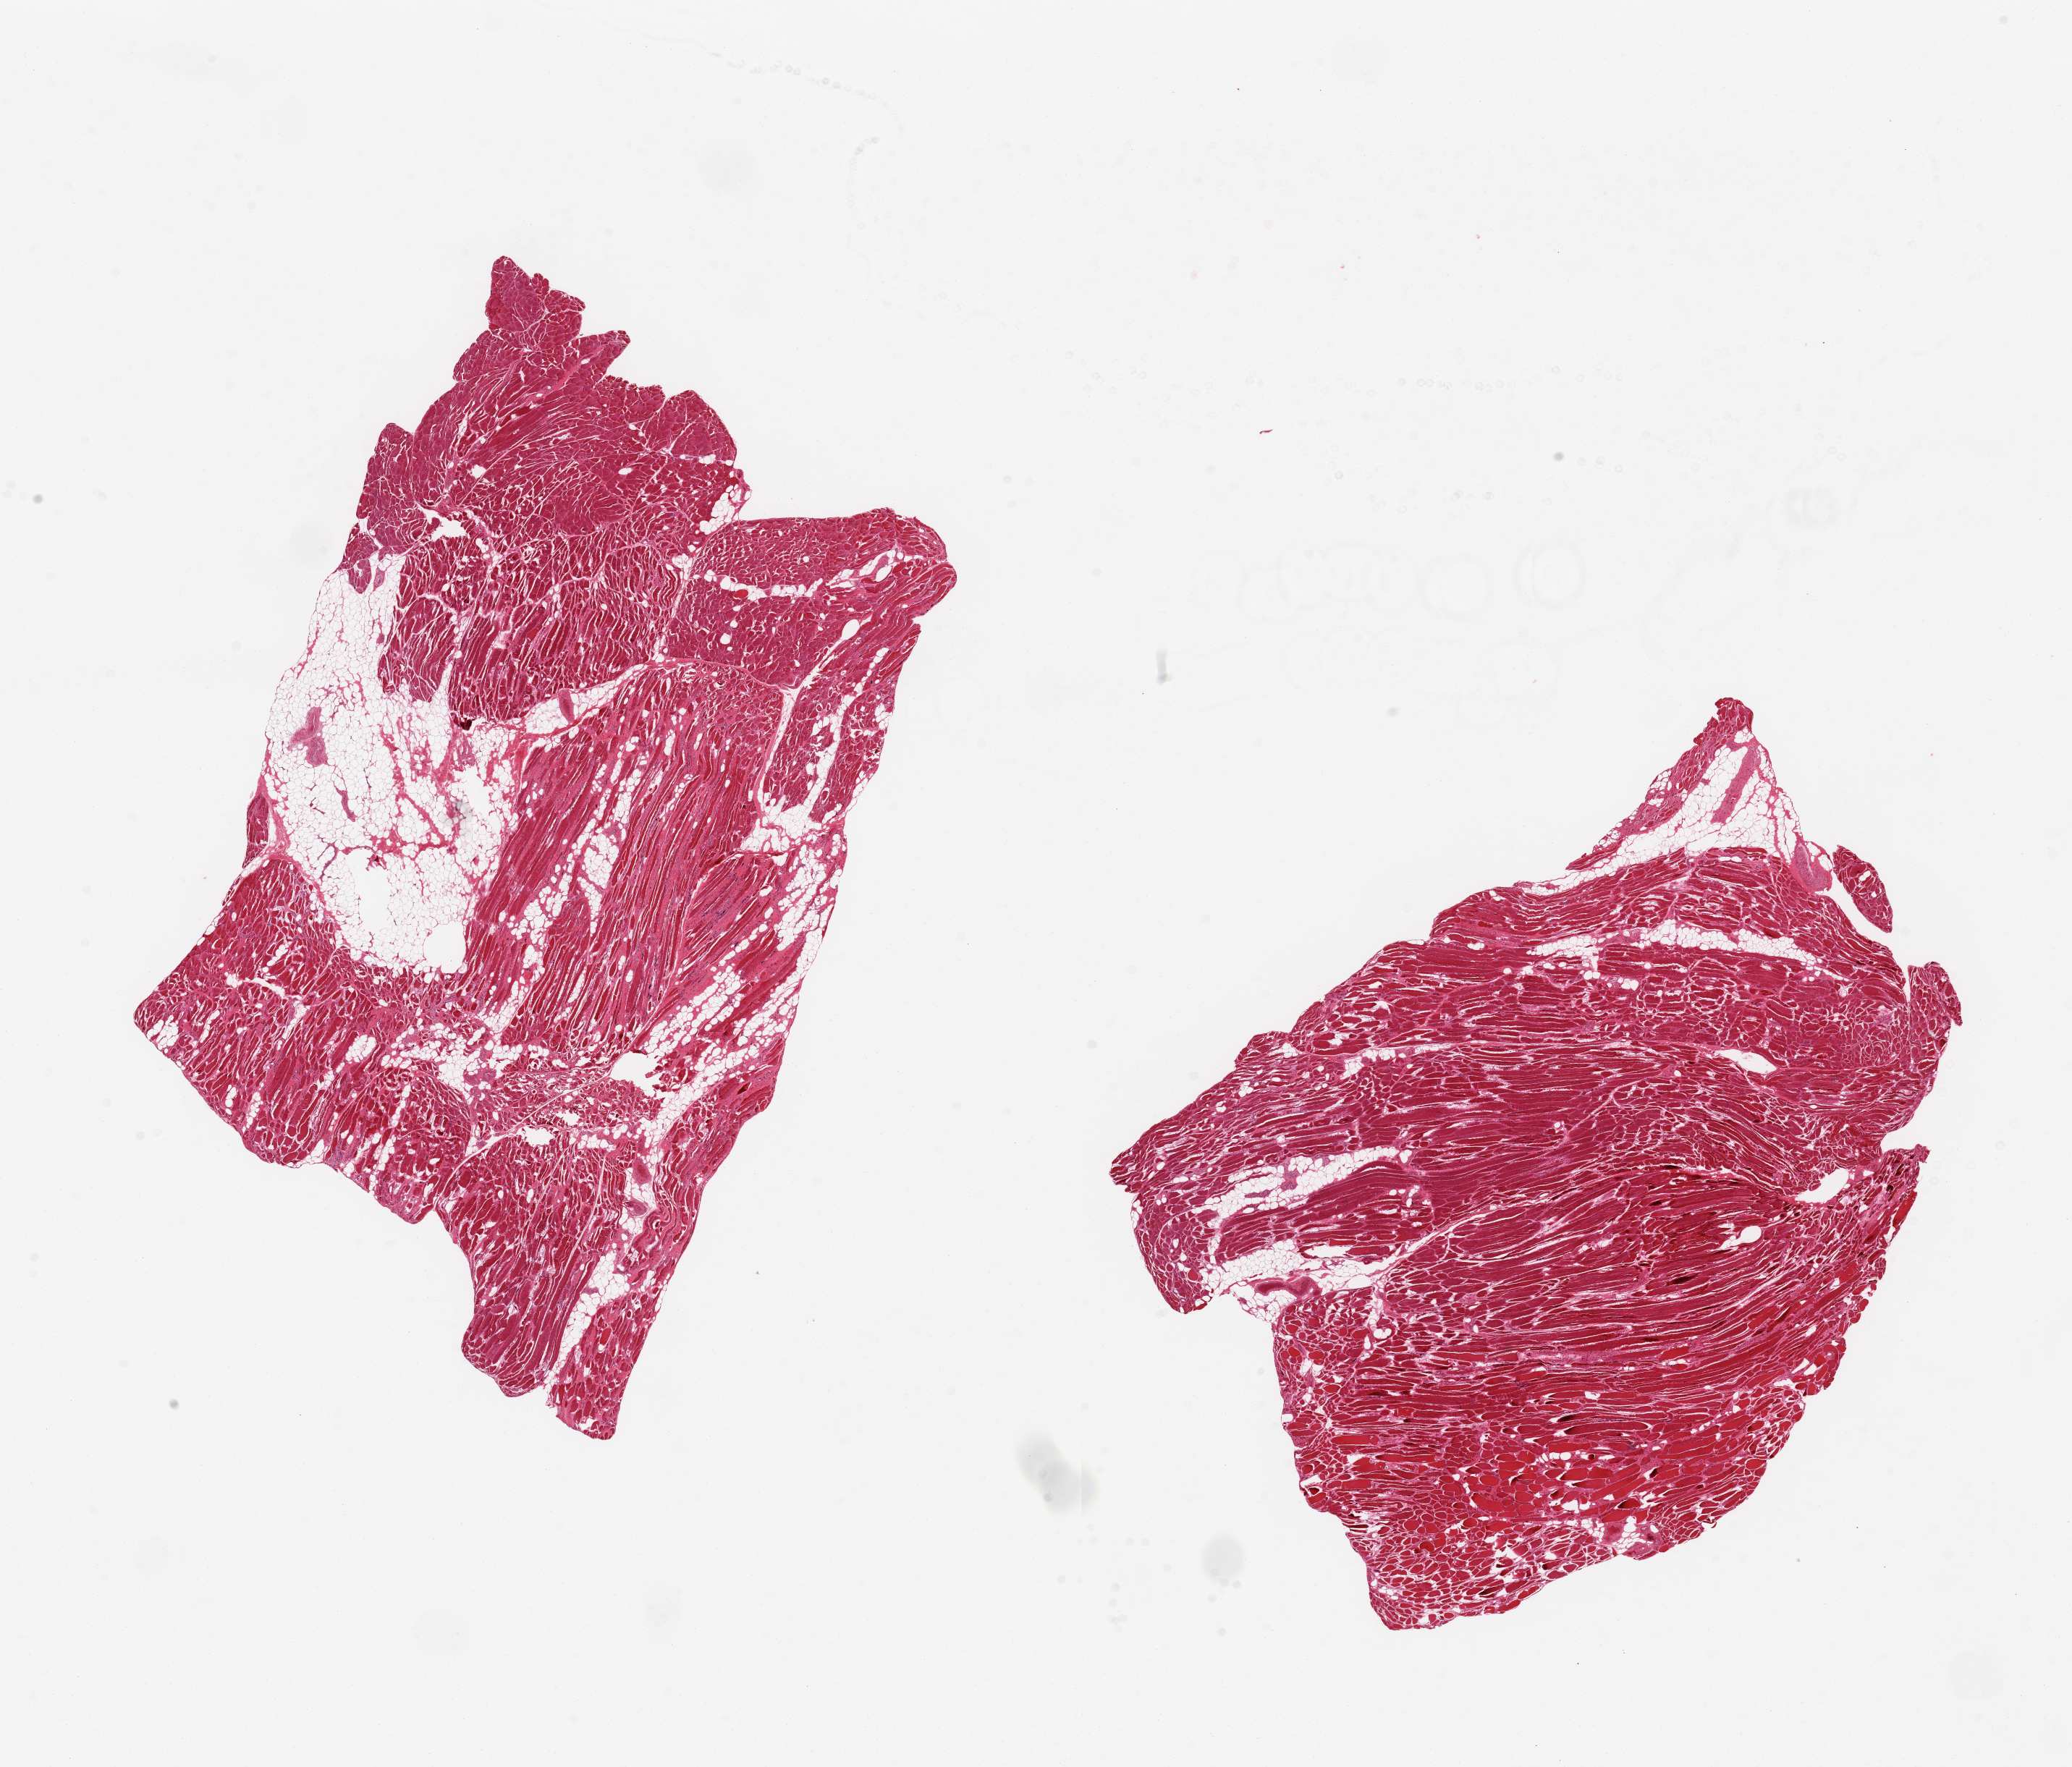
Digitized hematoxylin and eosin (H&E)-stained section, shown as a low-resolution overview of the whole scanned area (about 22.6 x 19.3 mm), PAXgene-fixed paraffin-embedded (PFPE) section, sampled site (target tissue): skeletal muscle, donor tissue sample. Donor: male.
Review note (as recorded): 2 pieces; 5% and 20% internal fat and nerve, some atrophy.